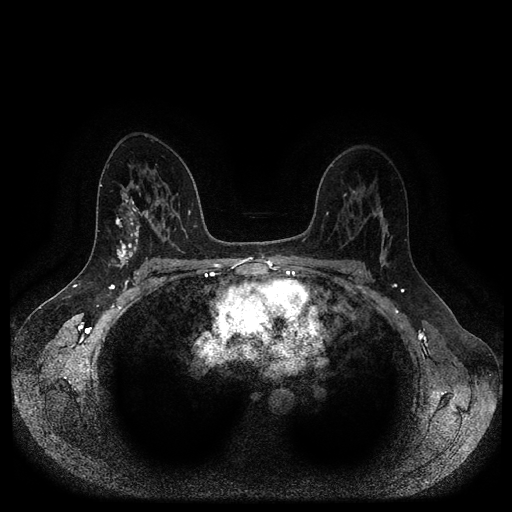
Breast MRI (dynamic contrast-enhanced, multi-phase), one axial slice; position 63 of 116 along the scan axis; dynamic contrast-enhanced series, time point 2 of 5 at this slice position (early post-contrast); 1.5 T; TE 2.6 ms, TR 5.3 ms; 2 mm slice thickness; 512 × 512 image matrix, field of view 360 × 360 mm. Patient: female, 45 years.
Structures marked on this image (semi-automatic segmentation, software-assisted and operator-edited):
- breast lesion (labelled benign in the annotation): box from (x=115, y=213) to (x=140, y=258) px
- breast lesion (labelled 'tumour' in the annotation; benign lesions carry a separate 'benign' label): (x=116, y=239)–(x=128, y=269)